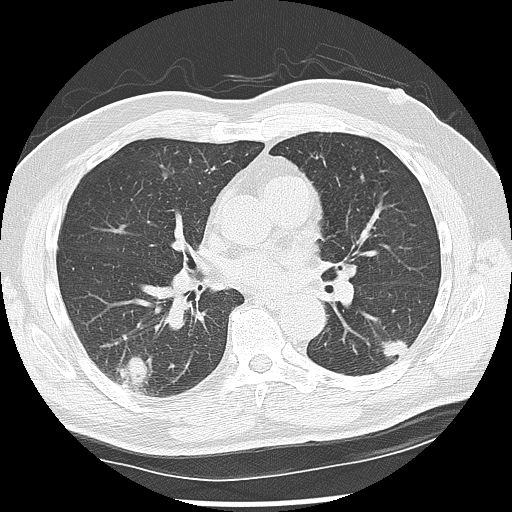
Low-dose screening chest CT, one axial slice. Position 66 of 142 along the scan axis. Reconstruction kernel LUNG. Lung window (W 1500 / L -600 HU). 2.5 mm slice thickness. 512 × 512 image matrix, field of view 360 × 360 mm.
Outlined on this slice (manually delineated by an expert):
- lesion 1 (nodule, lower lobe of left lung): bounding box (x1, y1, x2, y2) in pixels: (379, 339, 410, 358)
- lesion 2 (nodule, lower lobe of right lung): (118, 355, 149, 390)